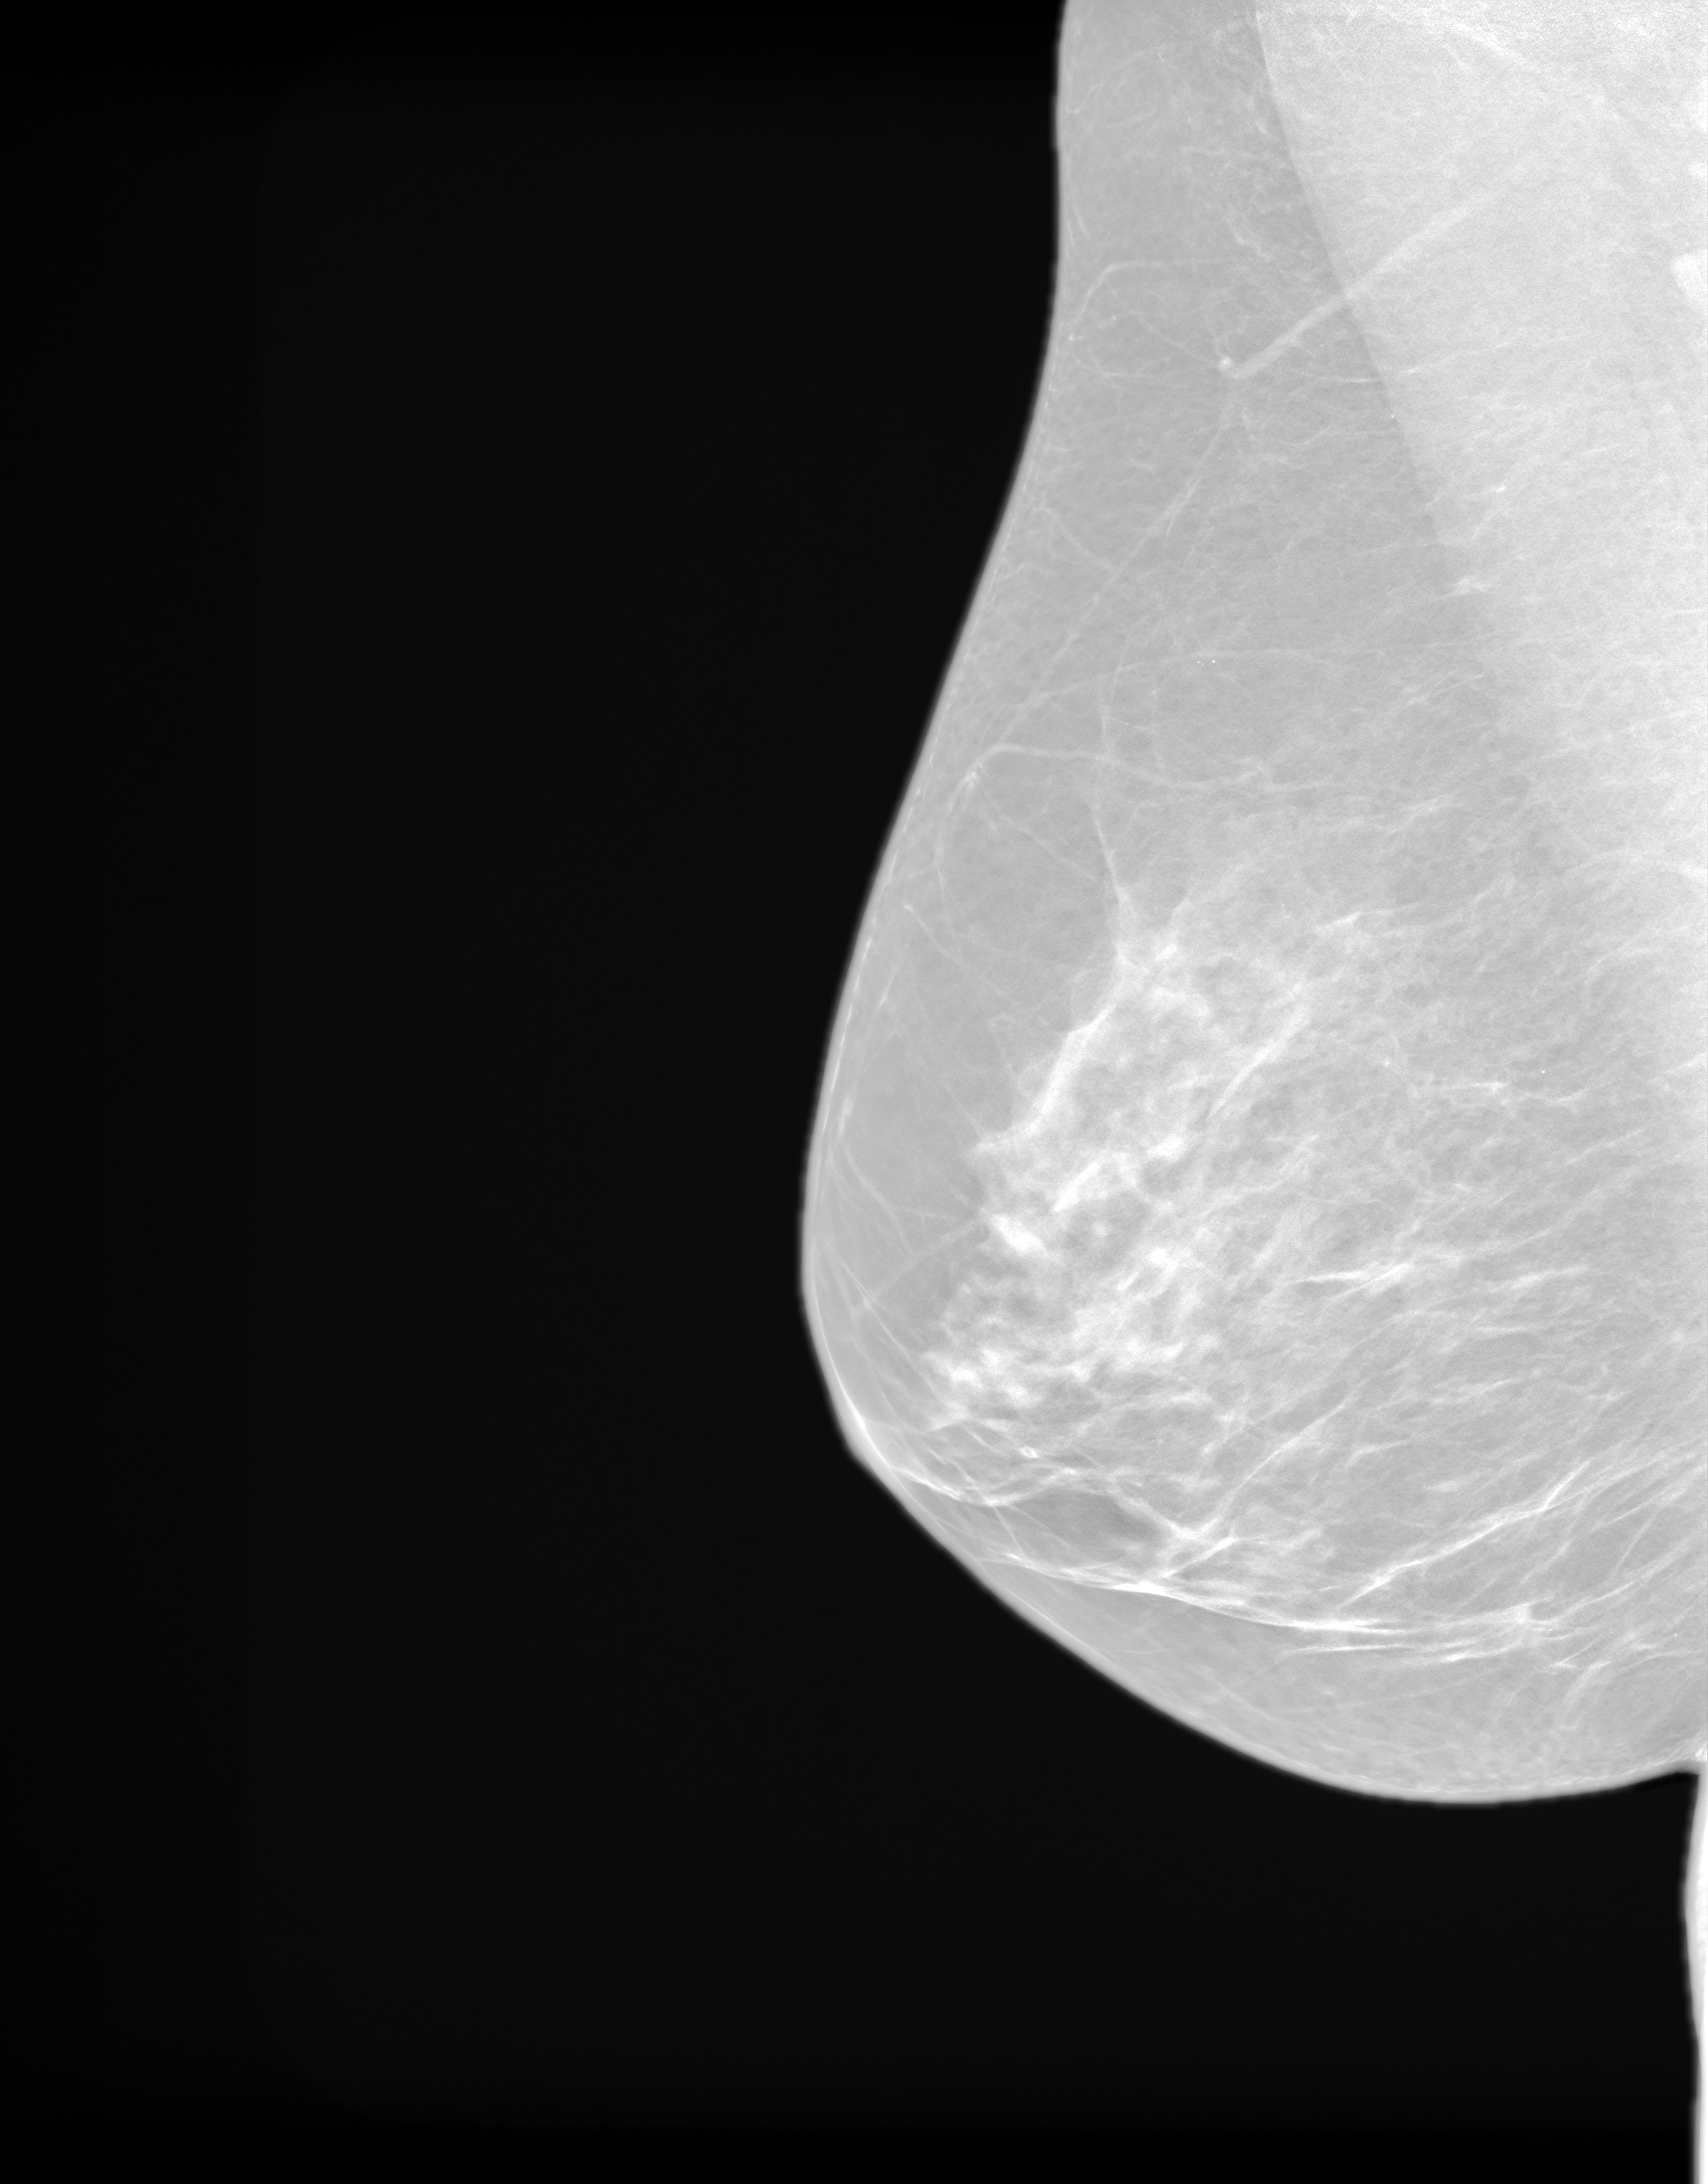
Synthesized 2-D mammogram reconstructed from digital breast tomosynthesis; right breast; mediolateral oblique (MLO) view; screening examination. Patient aged 57 years (female).
BI-RADS breast density category at the screening exam (both breasts, scale 1–4): 2. Final BI-RADS assessment for this screening round (tomosynthesis exam, both breasts): category 1. Recall: no recall after this screen.